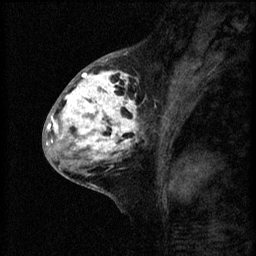
Breast MRI (dynamic contrast-enhanced), one sagittal slice; position 27 of 60 along the scan axis; 3 images stored at this slice position (order not interpretable as contrast timing); 1.5 T; TE 4.2 ms, TR 8.2 ms; 2 mm slice thickness; 256 × 256 image matrix, field of view 180 × 180 mm. Patient: female, 41 years.
Annotated regions visible in this slice (semi-automatically segmented with operator editing):
- analysis volume of interest (the breast-tissue region the enhancement analysis was run in; not a lesion): bounding box <53,62,160,175> (left, top, right, bottom; pixels)
- tumour enhancement mask (voxels above the 70 % enhancement threshold inside the analysis volume of interest): <53,70,139,161>